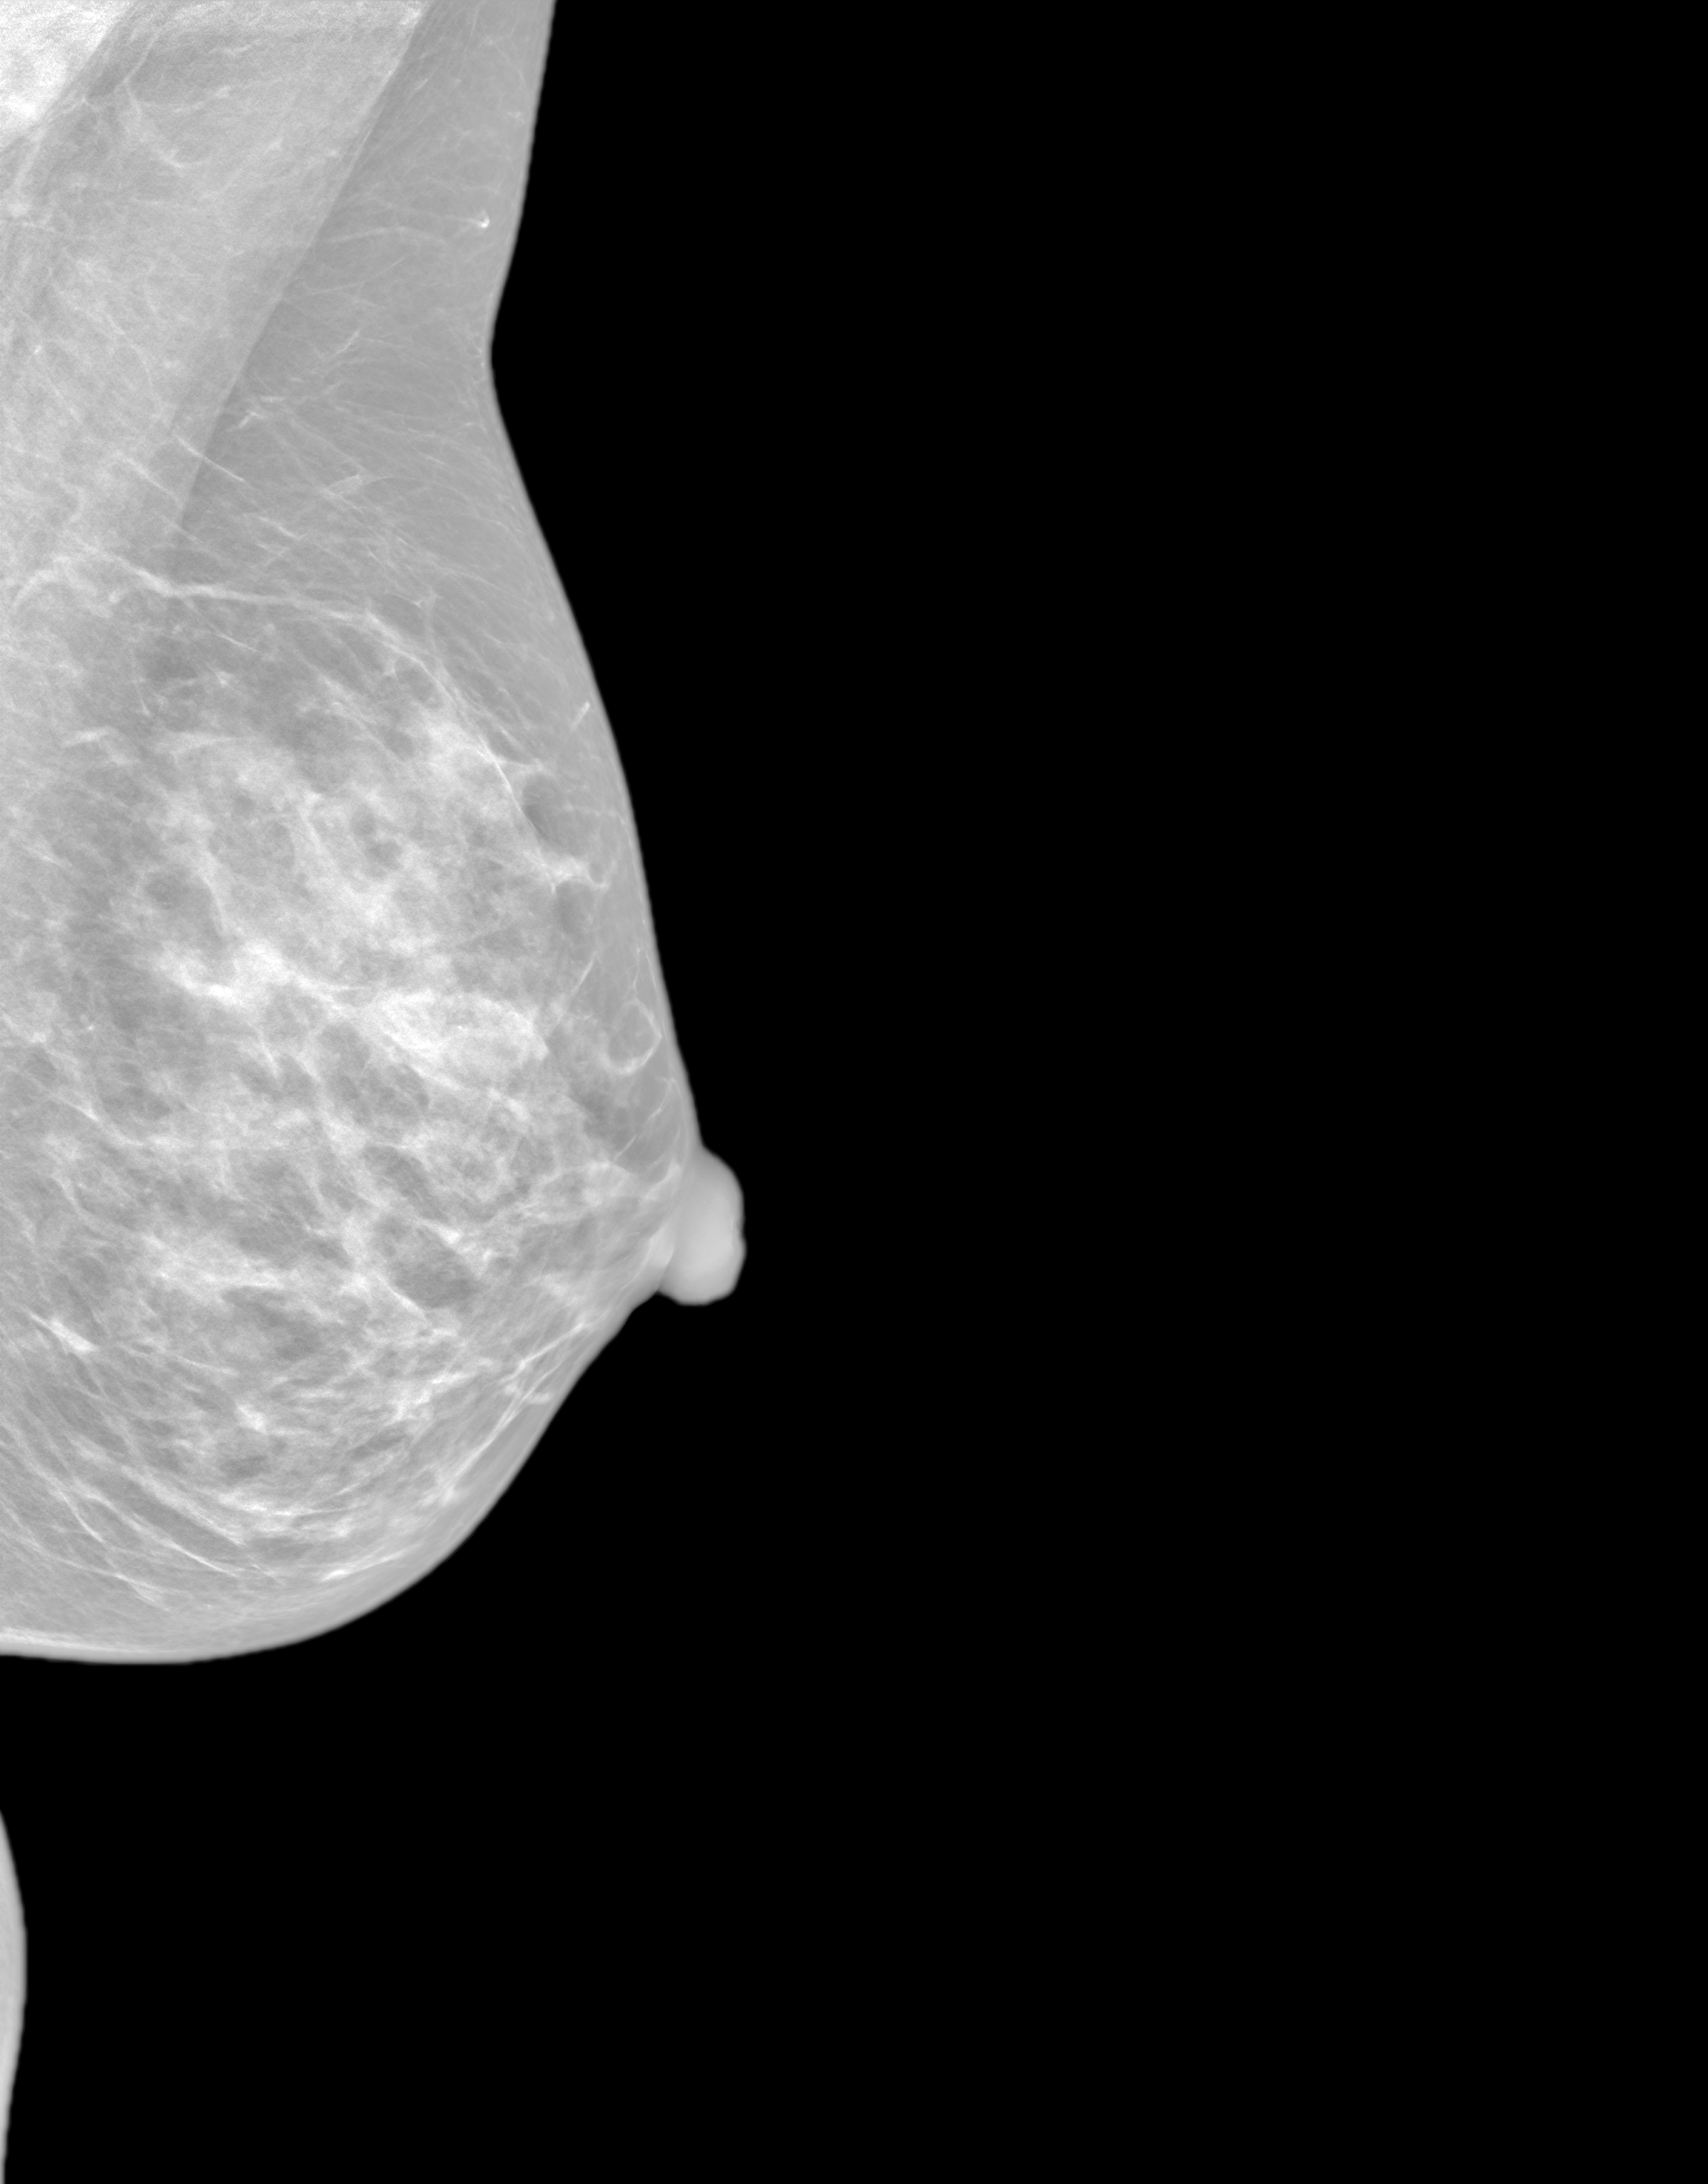
Synthesized 2-D mammogram reconstructed from digital breast tomosynthesis; left breast; medio-lateral oblique projection; screening examination. Patient aged 42 years (female).
Final BI-RADS category for the screening round (tomosynthesis exam, both breasts): category 1.